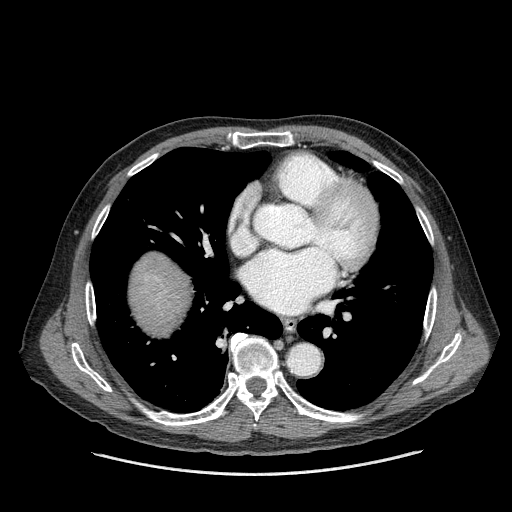
Contrast-enhanced abdominal CT (liver protocol), one axial slice. One of 2 acquisitions stored at this slice position. Soft-tissue window (W 400 / L 40 HU). 2.5 mm slice thickness. 512 × 512 image matrix, field of view 420 × 420 mm. Case-level facts recorded for this patient, not image findings: diagnosis: hepatocellular carcinoma (patient treated with transarterial chemoembolisation; whether this scan precedes or follows treatment is not stated here); TNM stage (as recorded): Stage-II; Child-Pugh class: A; tumour nodularity: multinodular.
Outlined on this slice (semi-automatically segmented with operator editing):
- liver parenchyma outside the tumour (the mass and vessels are separate outlines, so this box may not span the whole liver): bounding box (x1, y1, x2, y2) in pixels: (130, 252, 192, 334)
- mass: (140, 273, 165, 300)